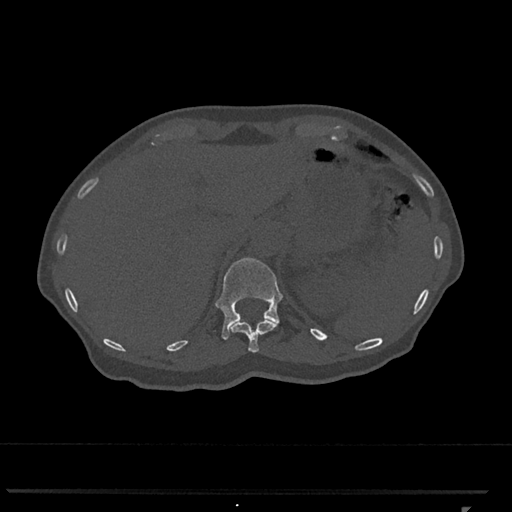
CT including the spine, one axial slice. Slice 487 of 793 in the series (ordered by position). 120 kVp. Bone window (W 1800 / L 400 HU). 0.5 mm slice thickness. 512 × 512 image matrix, field of view 380 × 380 mm. Female patient, age 62 years. Case-level facts recorded for this patient, not image findings: primary cancer: renal.
Structures marked on this image (semi-automatically segmented with operator editing):
- T11 vertebra: box from (x=230, y=319) to (x=277, y=353) px
- T12 vertebra: (x=215, y=257)–(x=283, y=340)